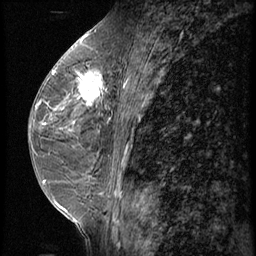
Breast MRI (dynamic contrast-enhanced), one sagittal slice; slice 29 of 62 in the series (ordered by position); 3 images stored at this slice position (order not interpretable as contrast timing); 1.5 T; TE 4.2 ms, TR 9 ms; 256 × 256 image matrix, field of view 180 × 180 mm. Patient: female, 44 years. Case-level facts recorded for this patient, not image findings: setting: breast cancer imaged before/during neoadjuvant chemotherapy; receptor status: triple-negative.
Structures marked on this image (semi-automatic segmentation, software-assisted and operator-edited):
- analysis volume of interest (the breast-tissue region the enhancement analysis was run in; not a lesion): bounding box (x1, y1, x2, y2) in pixels: (67, 64, 116, 125)
- tumour enhancement mask (voxels above the 140 % enhancement threshold inside the analysis volume of interest): (68, 73, 111, 121)